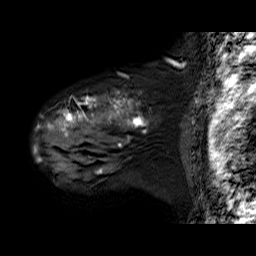
Breast MRI (dynamic contrast-enhanced), one sagittal slice; position 51 of 60 along the scan axis; dynamic contrast-enhanced series, time point 2 of 6 at this slice position (early post-contrast); 1.5 T; TE 6.3 ms, TR 32.9 ms; 4 mm slice thickness; 256 × 256 image matrix, field of view 200 × 200 mm. Female patient. Case-level facts recorded for this patient, not image findings: setting: breast cancer imaged before/during neoadjuvant chemotherapy; receptor status: HER2-positive.
Outlined on this slice (semi-automatically segmented with operator editing):
- analysis volume of interest (the breast-tissue region the enhancement analysis was run in; not a lesion): bounding box (x1, y1, x2, y2) in pixels: (34, 90, 182, 180)
- tumour enhancement mask (voxels above the 100 % enhancement threshold inside the analysis volume of interest): (34, 97, 149, 174)